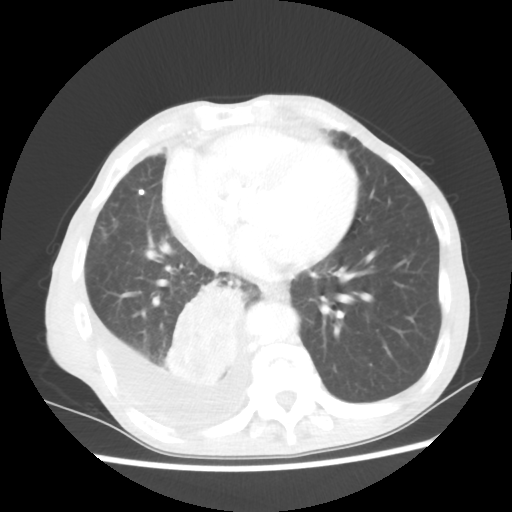
Chest CT, one axial slice. Slice 22 of 60 in the series (ordered by position). Lung window (W 1500 / L -600 HU). 5 mm slice thickness. 512 × 512 image matrix. Male patient, age 76 years. Case-level facts recorded for this patient, not image findings: clinical TNM (as recorded): T3 N3 M1a; histopathological grade: G3.
Structures marked on this image (bounding box drawn by a radiologist):
- lung tumour (recorded histology: squamous cell carcinoma): bounding box <161,274,252,389> (left, top, right, bottom; pixels)